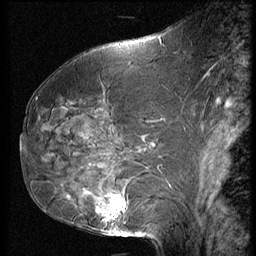
Breast MRI (dynamic contrast-enhanced), one sagittal slice; position 28 of 62 along the scan axis; 3 images stored at this slice position (order not interpretable as contrast timing); 1.5 T; TE 4.2 ms, TR 9 ms; 2.5 mm slice thickness; 256 × 256 image matrix. Female patient, age 50 years. Case-level facts recorded for this patient, not image findings: setting: breast cancer imaged before/during neoadjuvant chemotherapy; receptor status: HR-positive, HER2-negative.
Annotated regions visible in this slice (semi-automatically segmented with operator editing):
- analysis volume of interest (the breast-tissue region the enhancement analysis was run in; not a lesion): bounding box (x1, y1, x2, y2) in pixels: (59, 125, 139, 237)
- tumour enhancement mask (voxels above the 140 % enhancement threshold inside the analysis volume of interest): (97, 194, 126, 221)